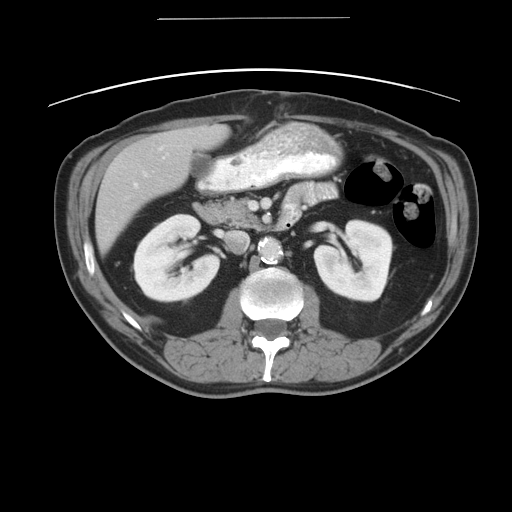
Contrast-enhanced abdominal CT, one axial slice; slice 19 of 49 in the series (ordered by position); reconstruction kernel STANDARD; 120 kVp; intravenous contrast given; soft-tissue window (W 400 / L 40 HU); 5 mm slice thickness; 512 × 512 image matrix, field of view 413 × 413 mm. Male patient, age 57 years. Case-level facts recorded for this patient, not image findings: diagnosis: colorectal cancer liver metastases, imaged before liver resection; multiple liver metastases: yes; largest metastasis: 4 cm; disease in both lobes: no.
Structures marked on this image (outlined manually by an expert reader):
- hepatic veins: bounding box [x1, y1, x2, y2] px = [143, 172, 146, 175]
- liver: [95, 125, 226, 253]
- planned liver remnant (the part of the liver to remain after resection): [217, 128, 225, 140]
- portal vein (with intrahepatic branches): [134, 183, 136, 185]